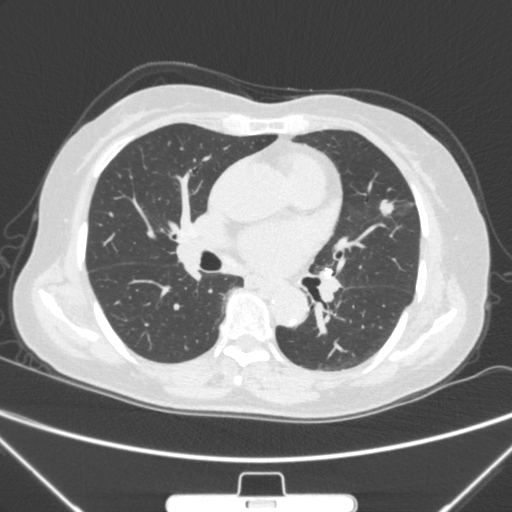
Chest CT, one axial slice; slice 148 of 300 in the series (ordered by position); lung window (W 1500 / L -600 HU); 1 mm slice thickness; 512 × 512 image matrix, field of view 350 × 350 mm. Patient: female, 70 years. Case-level facts recorded for this patient, not image findings: clinical TNM (as recorded): T1b N0 M0; histopathological grade: G2.
Outlined on this slice (rectangle marked by the reading radiologist):
- lung tumour (recorded histology: adenocarcinoma): box from (x=371, y=186) to (x=396, y=222) px